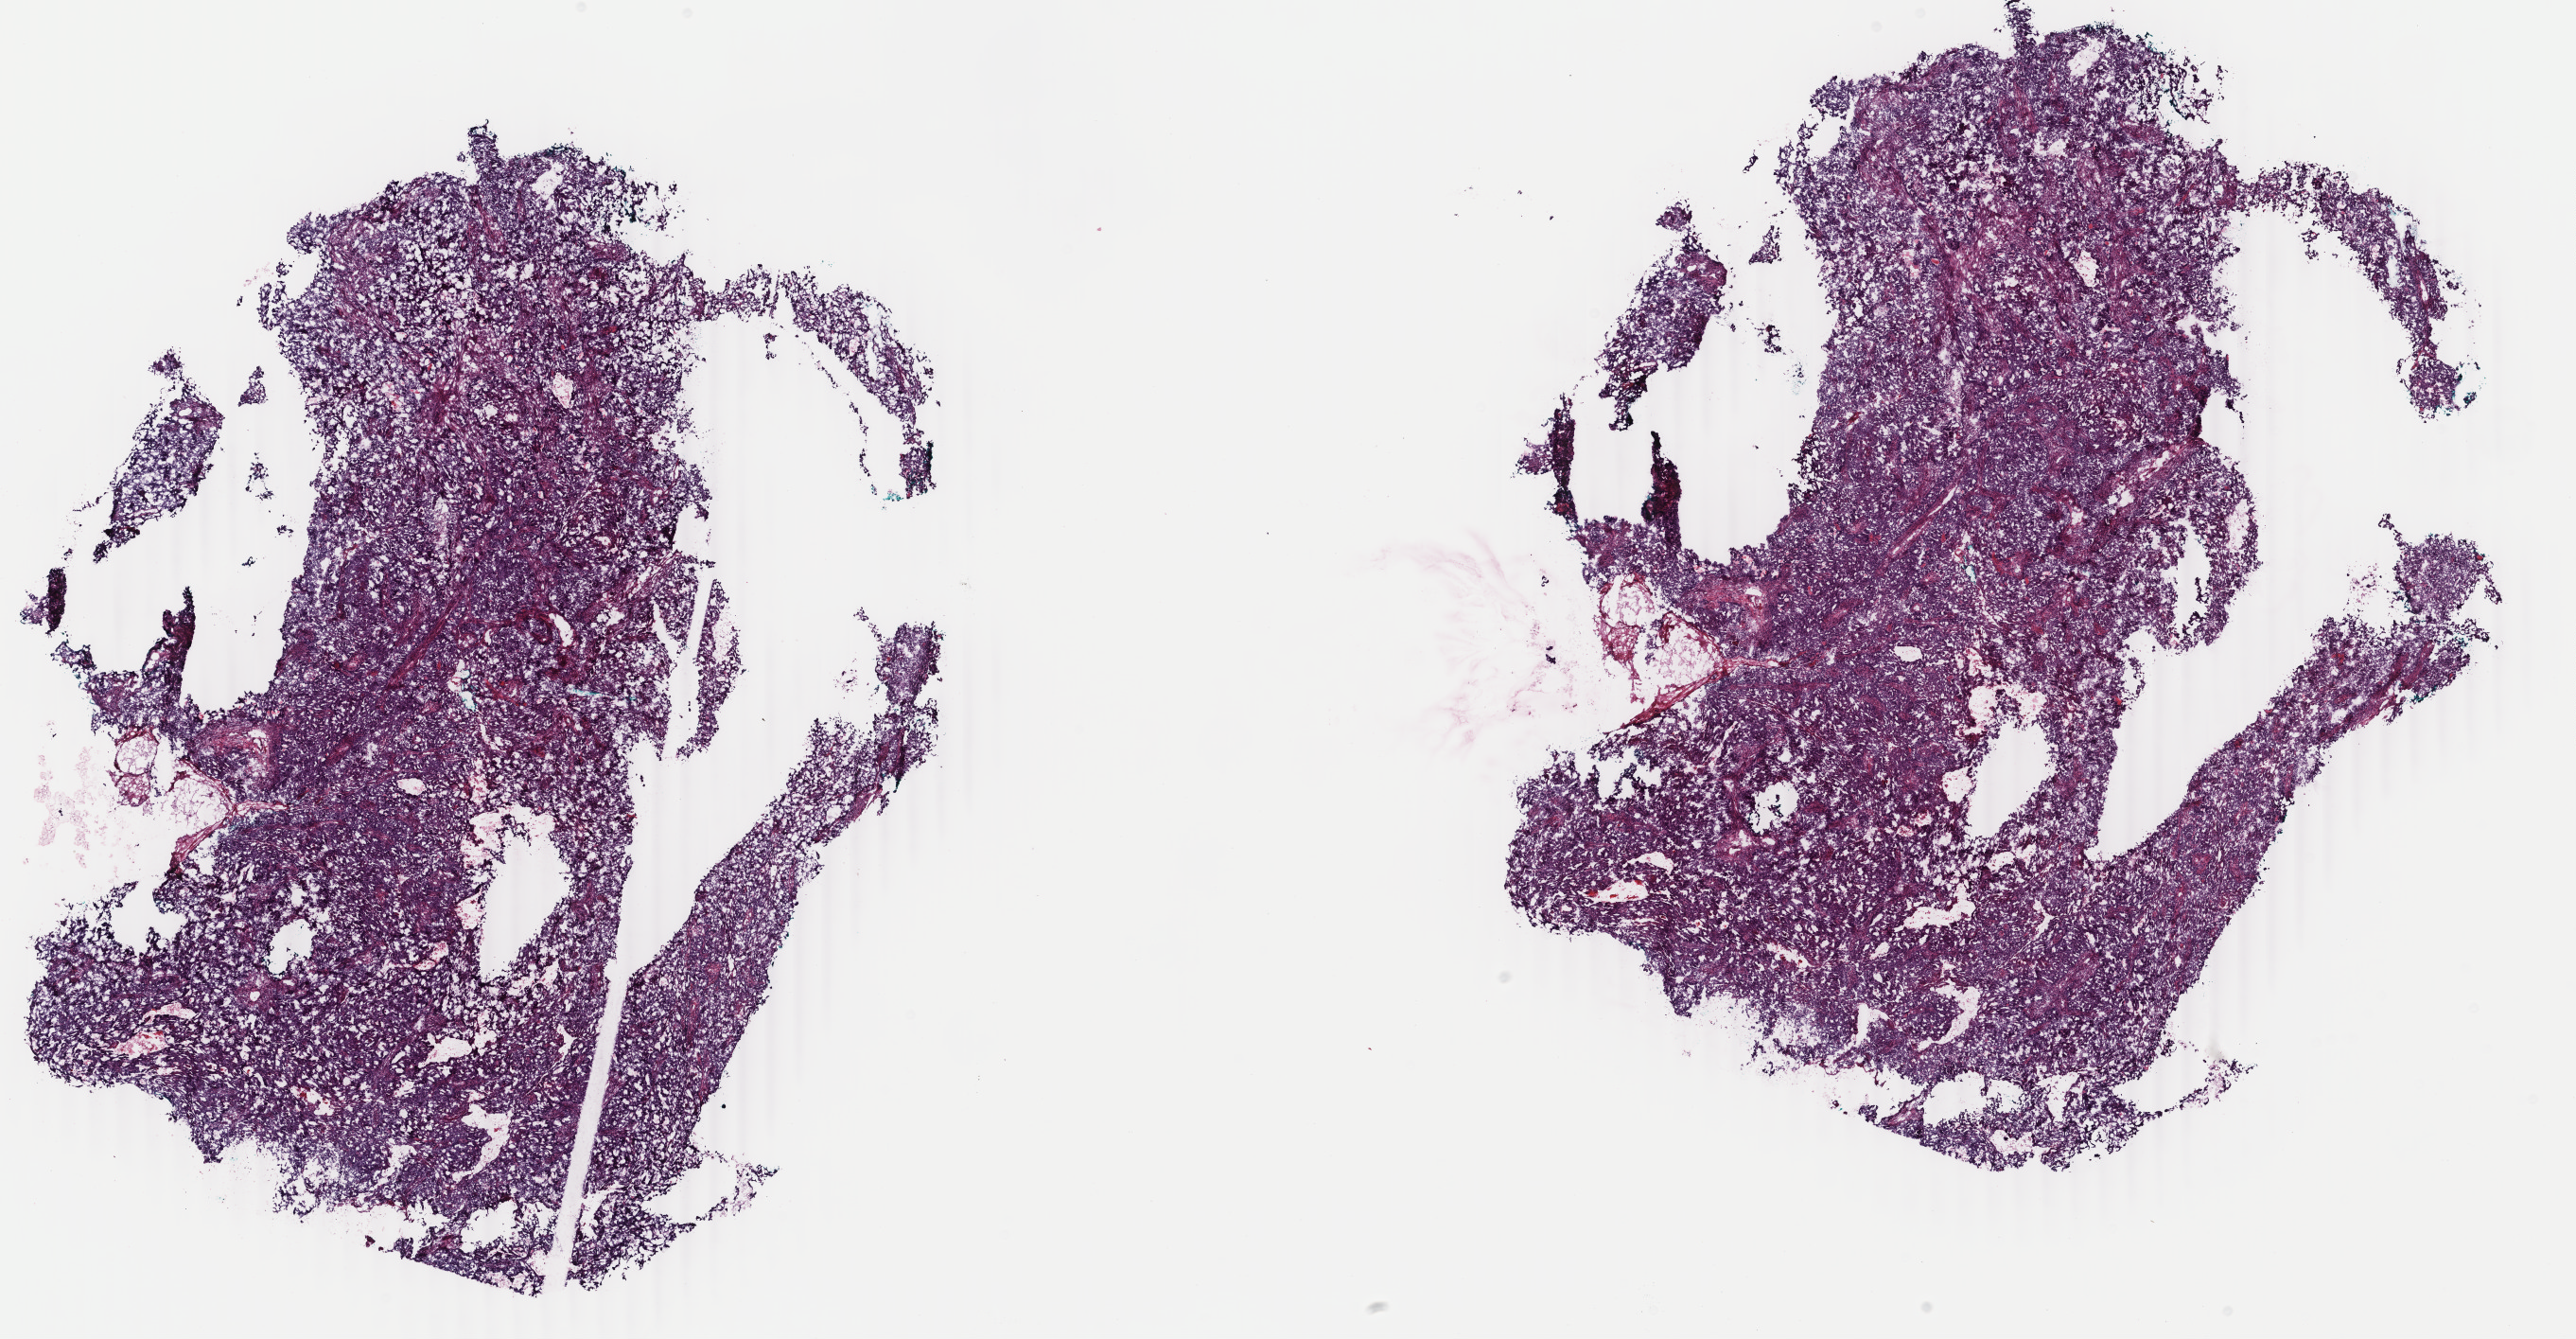
Whole-slide histology image, Hematoxylin and eosin (H&E) stained, low-resolution overview of the scanned area, about 21.7 x 11.3 mm (from a 40x scan); frozen section from the bottom of the tissue portion; uterus, primary tumour sample. Patient: female, age at initial diagnosis 62 years. Histologic grade: G2 (moderately differentiated). Pathologist review of this section (percent, as recorded): tumour cells 70%, tumour nuclei 70%, normal cells 0%, stromal cells 25%, necrosis 5%. Infiltration values recorded for this section: lymphocyte infiltration 80%, monocyte infiltration 0%, neutrophil infiltration 20%.
• lymph nodes positive (case pathology): 0 of 5 examined
• FIGO stage: IIB
• diagnosis: Endometrioid adenocarcinoma, NOS (endometrium)